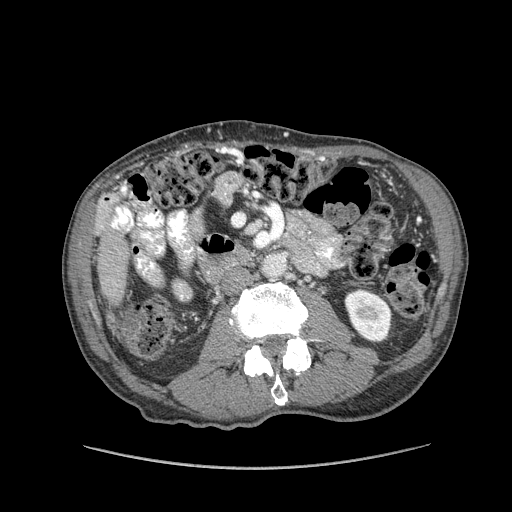
Contrast-enhanced abdominal CT (liver protocol), one axial slice. Position 13 of 162 along the scan axis. 100 kVp. Soft-tissue window (W 400 / L 40 HU). 2.5 mm slice thickness. 512 × 512 image matrix, field of view 400 × 400 mm. From the clinical record (not read from this slice): diagnosis: hepatocellular carcinoma (patient treated with transarterial chemoembolisation; whether this scan precedes or follows treatment is not stated here); TNM stage (as recorded): Stage-IIIA; Child-Pugh class: A; tumour nodularity: multinodular.
Structures marked on this image (semi-automatic segmentation, software-assisted and operator-edited):
- liver parenchyma outside the tumour (the mass and vessels are separate outlines, so this box may not span the whole liver): bounding box [x1, y1, x2, y2] px = [95, 200, 128, 306]